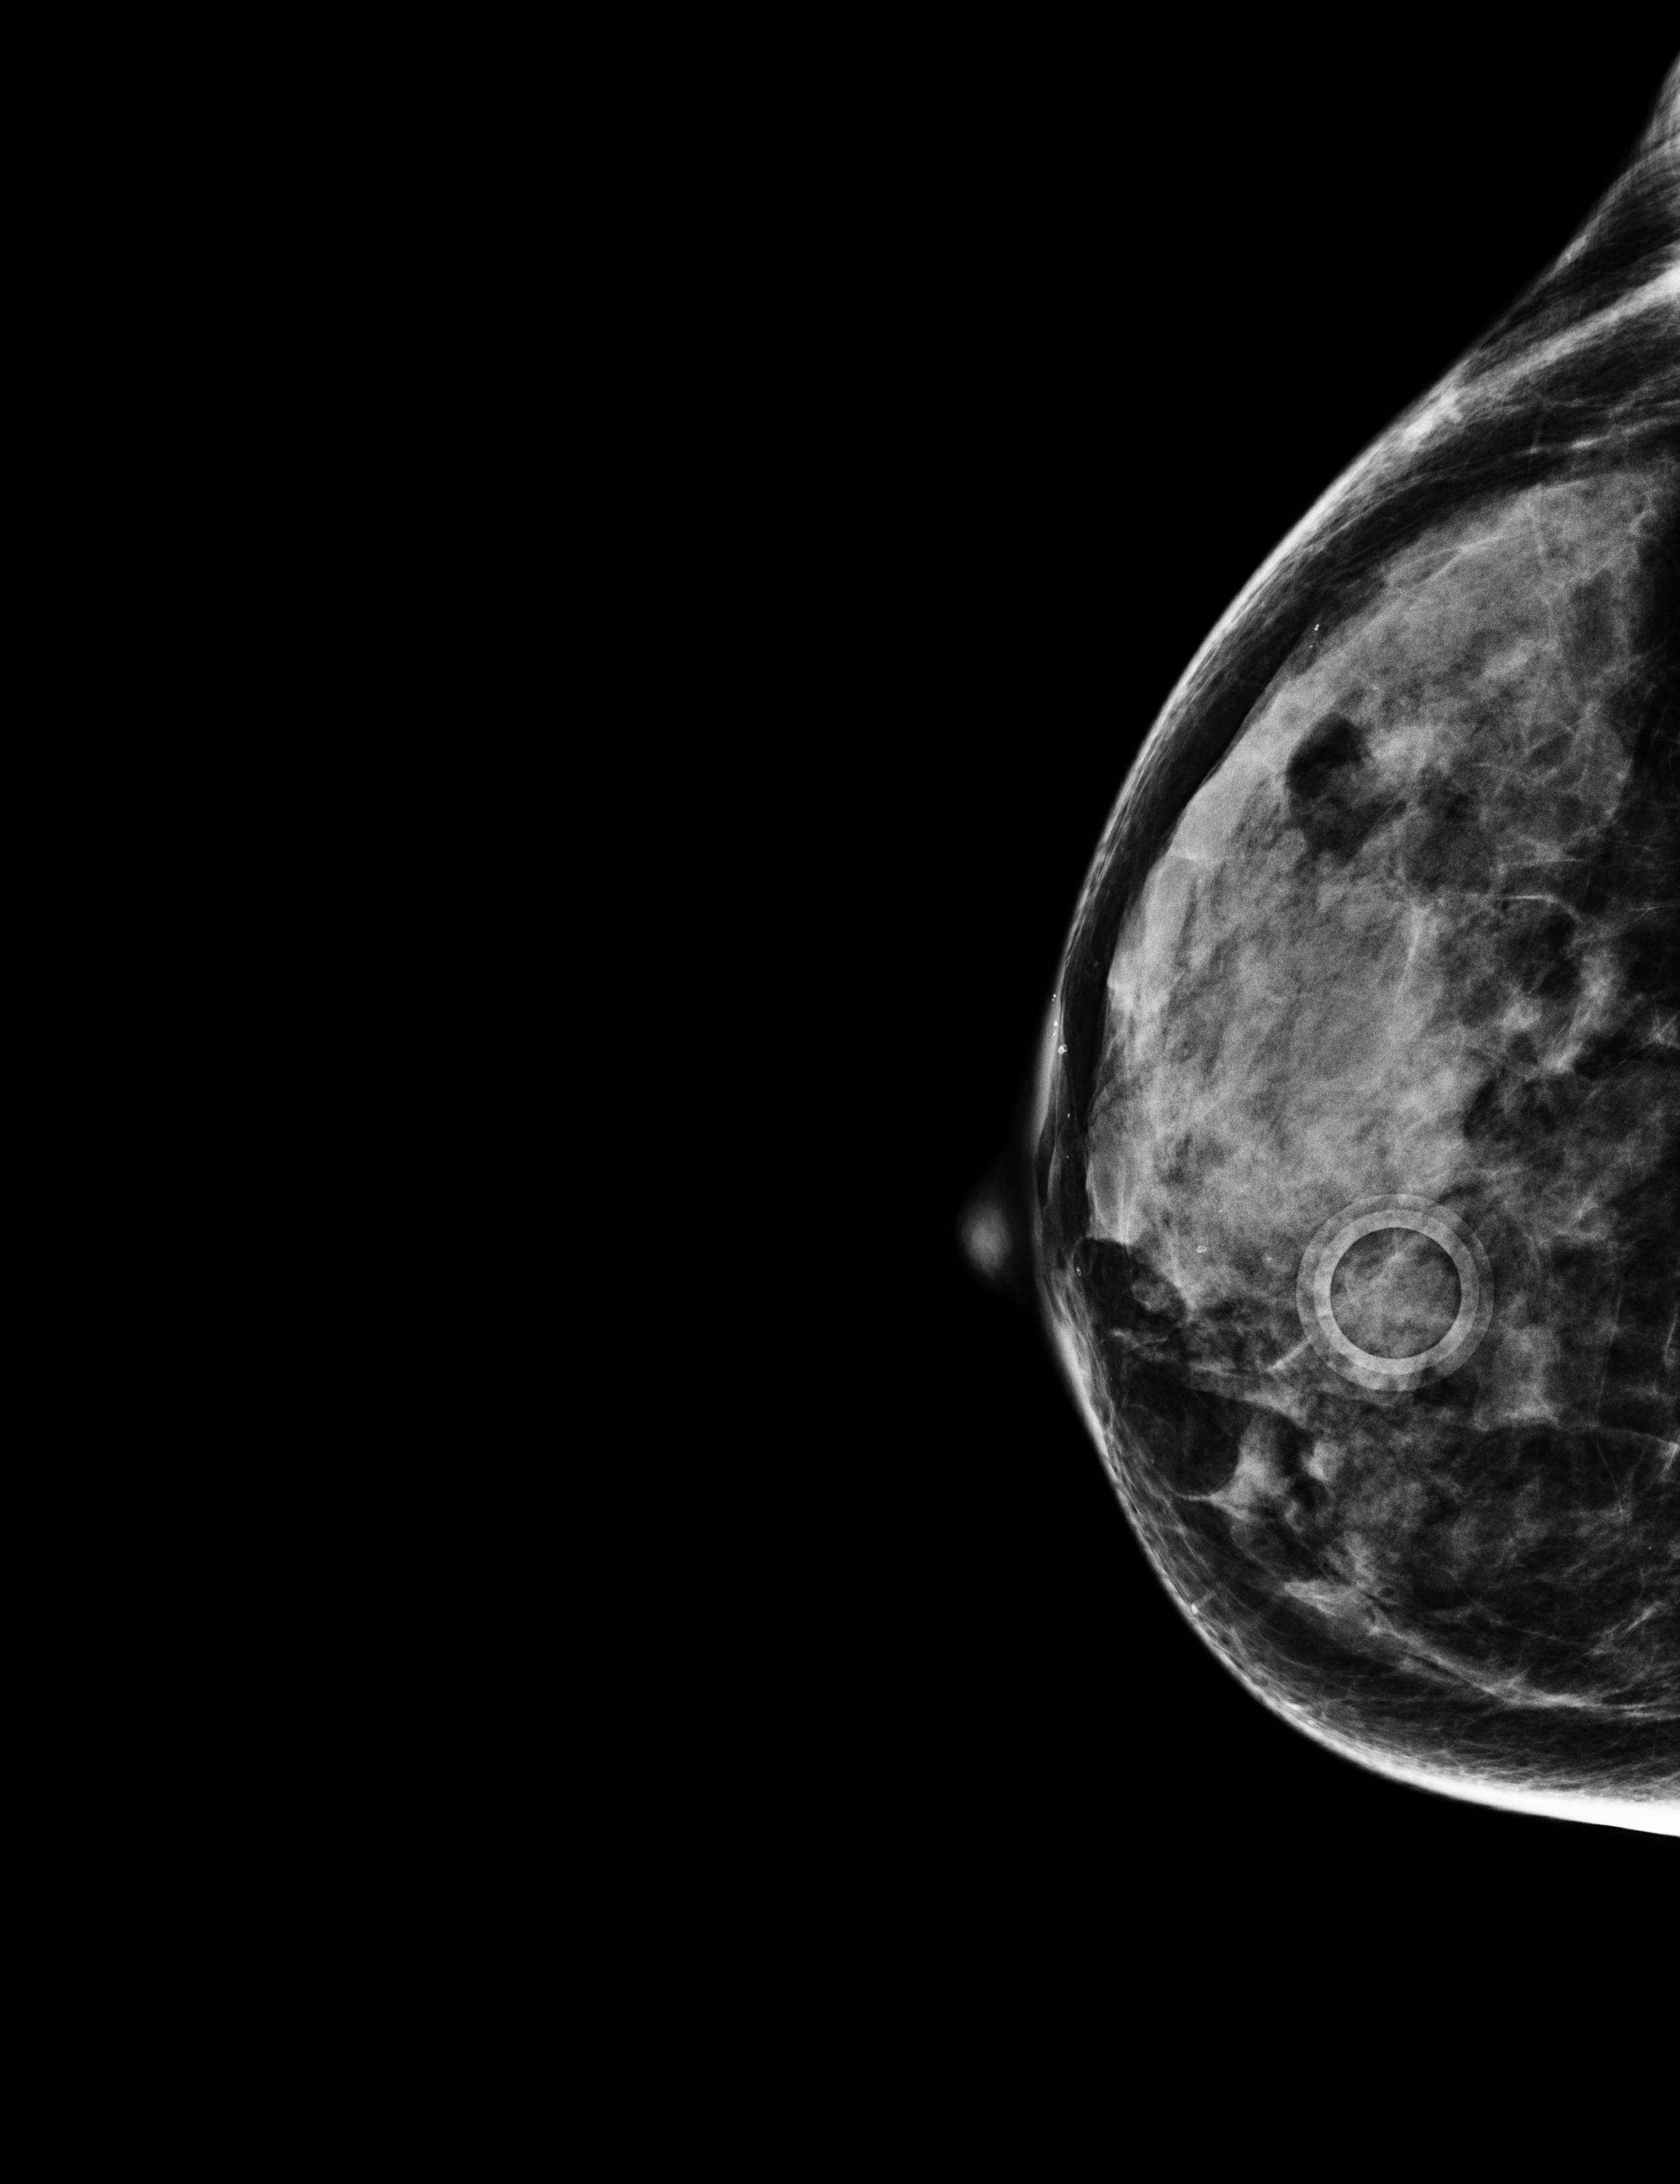
Annual screening mammography examination. Female patient, age 57 years.
Image type: full-field digital mammogram. Breast: right. Projection: CC view.